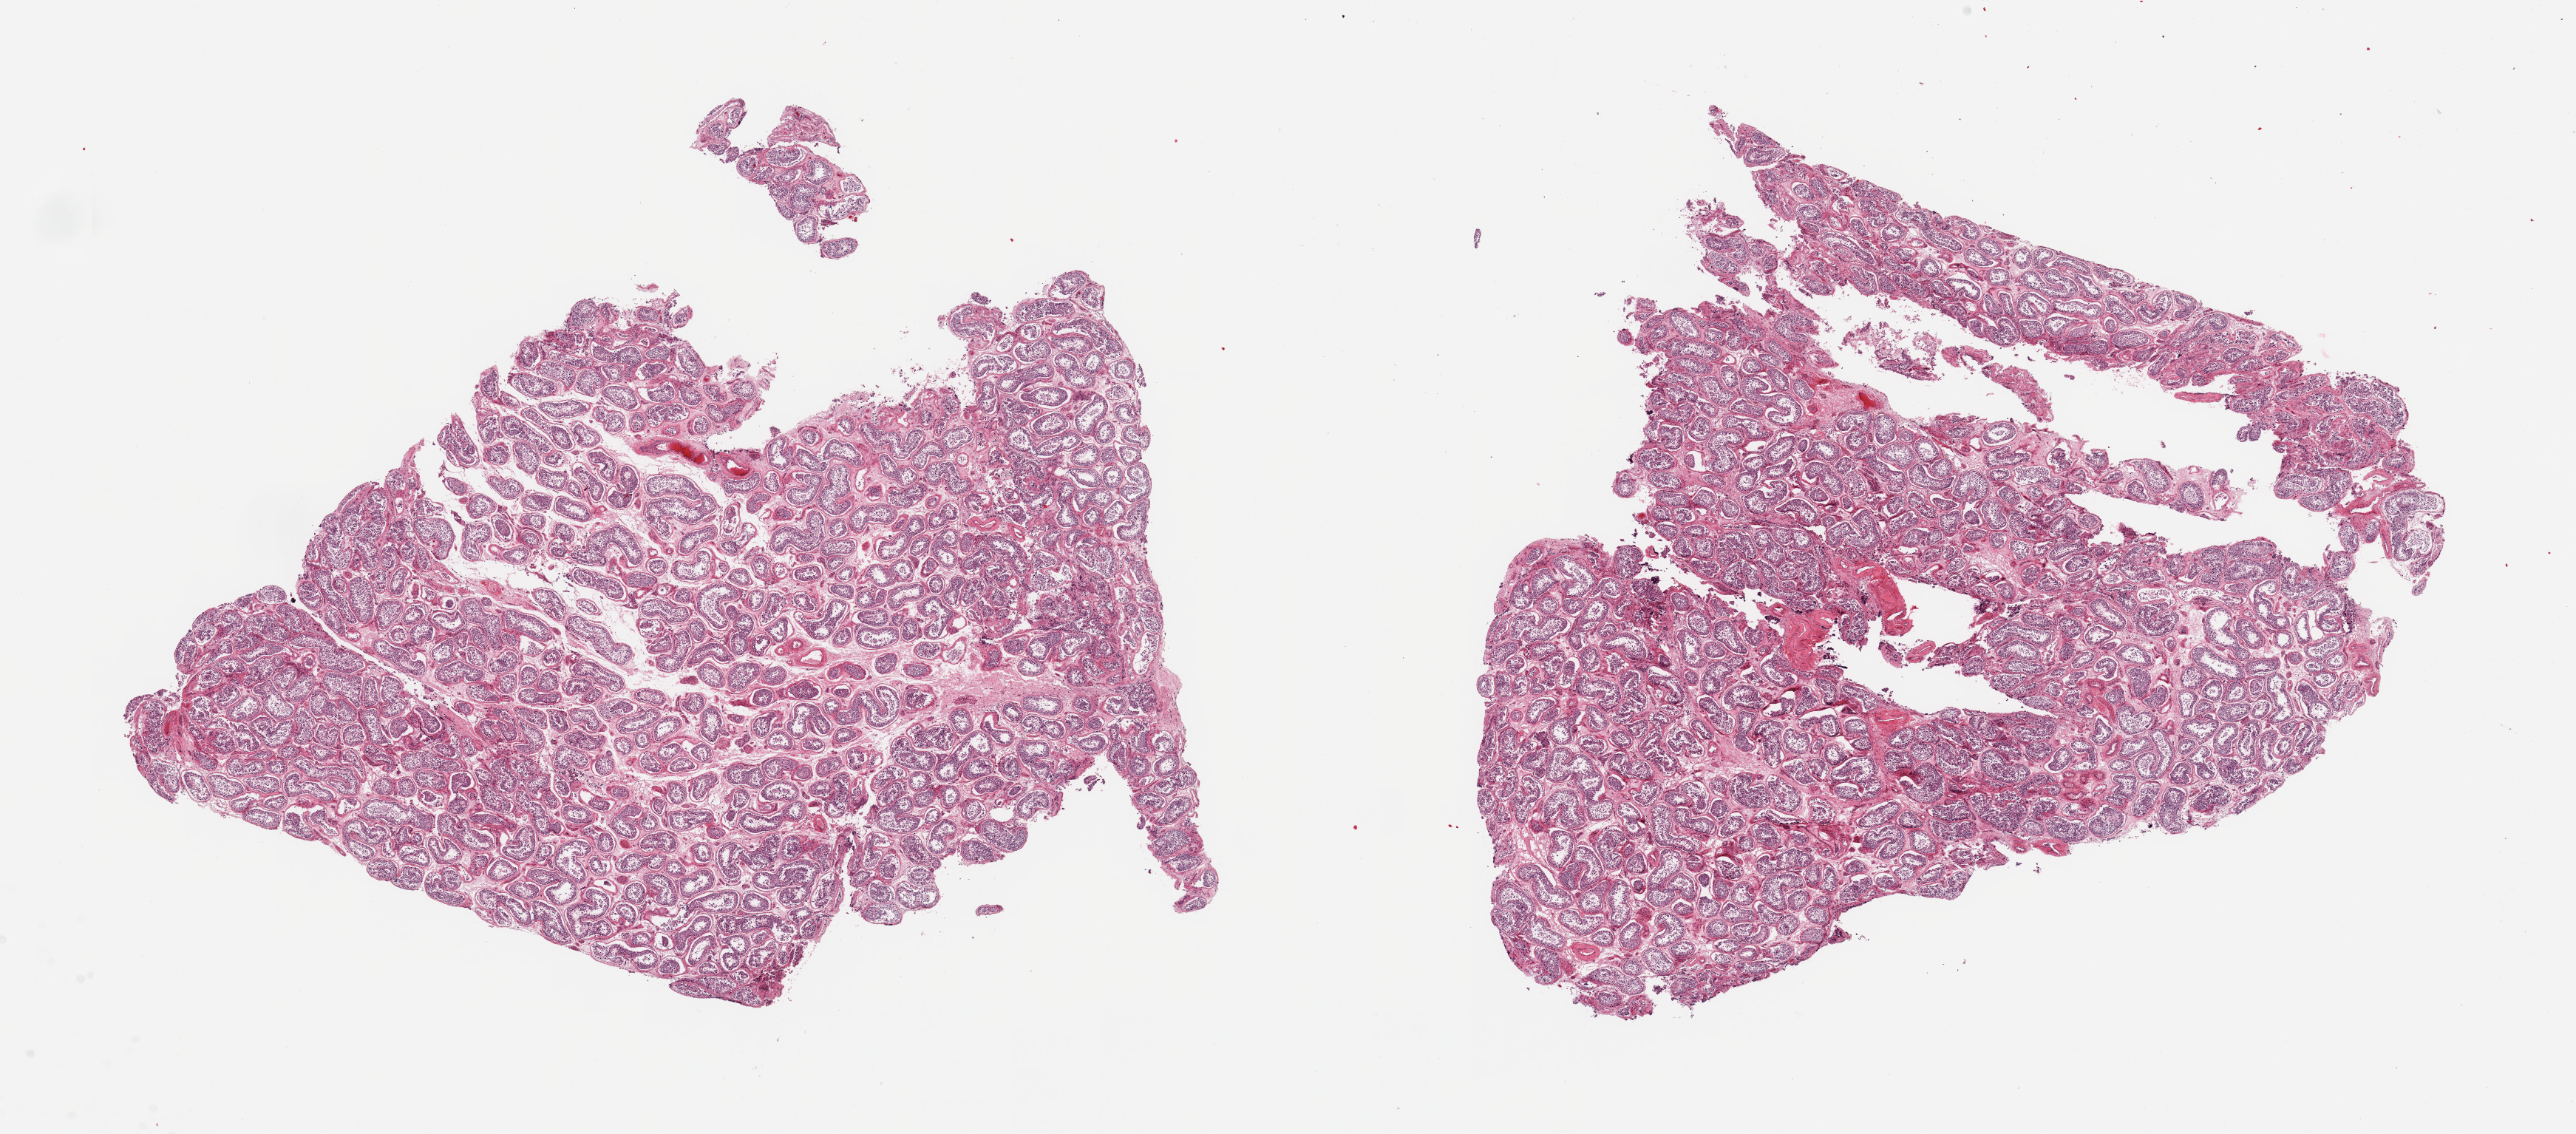
Whole-slide image, hematoxylin and eosin (H&E) stain, brightfield — whole scanned area (about 27.6 x 12.1 mm) shown as a low-resolution overview. PAXgene-fixed paraffin-embedded (PFPE) section. Sampled site (target tissue): testis. Donor tissue sample. Donor: male.
Reviewer comment on this tissue sample: 2 pieces; spermatogenesis is present.